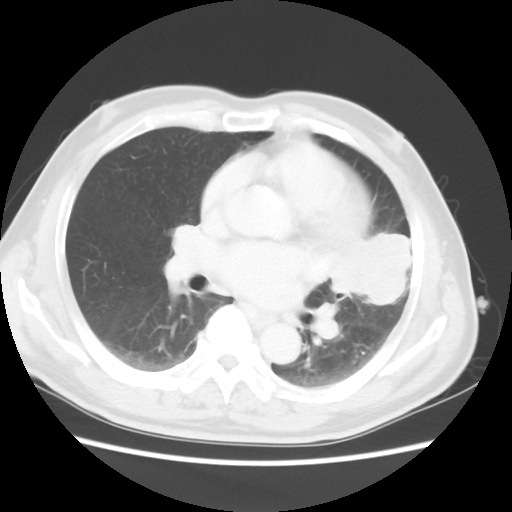
Chest CT, one axial slice. Position 25 of 50 along the scan axis. Reconstruction kernel STANDARD. 120 kVp. Lung window (W 1500 / L -600 HU). 5 mm slice thickness. 512 × 512 image matrix. Male patient, age 69 years. From the clinical record (not read from this slice): clinical TNM (as recorded): T3 N1 M1a.
Outlined on this slice (rectangle marked by the reading radiologist):
- lung tumour (recorded histology: squamous cell carcinoma): bounding box <333,233,420,309> (left, top, right, bottom; pixels)